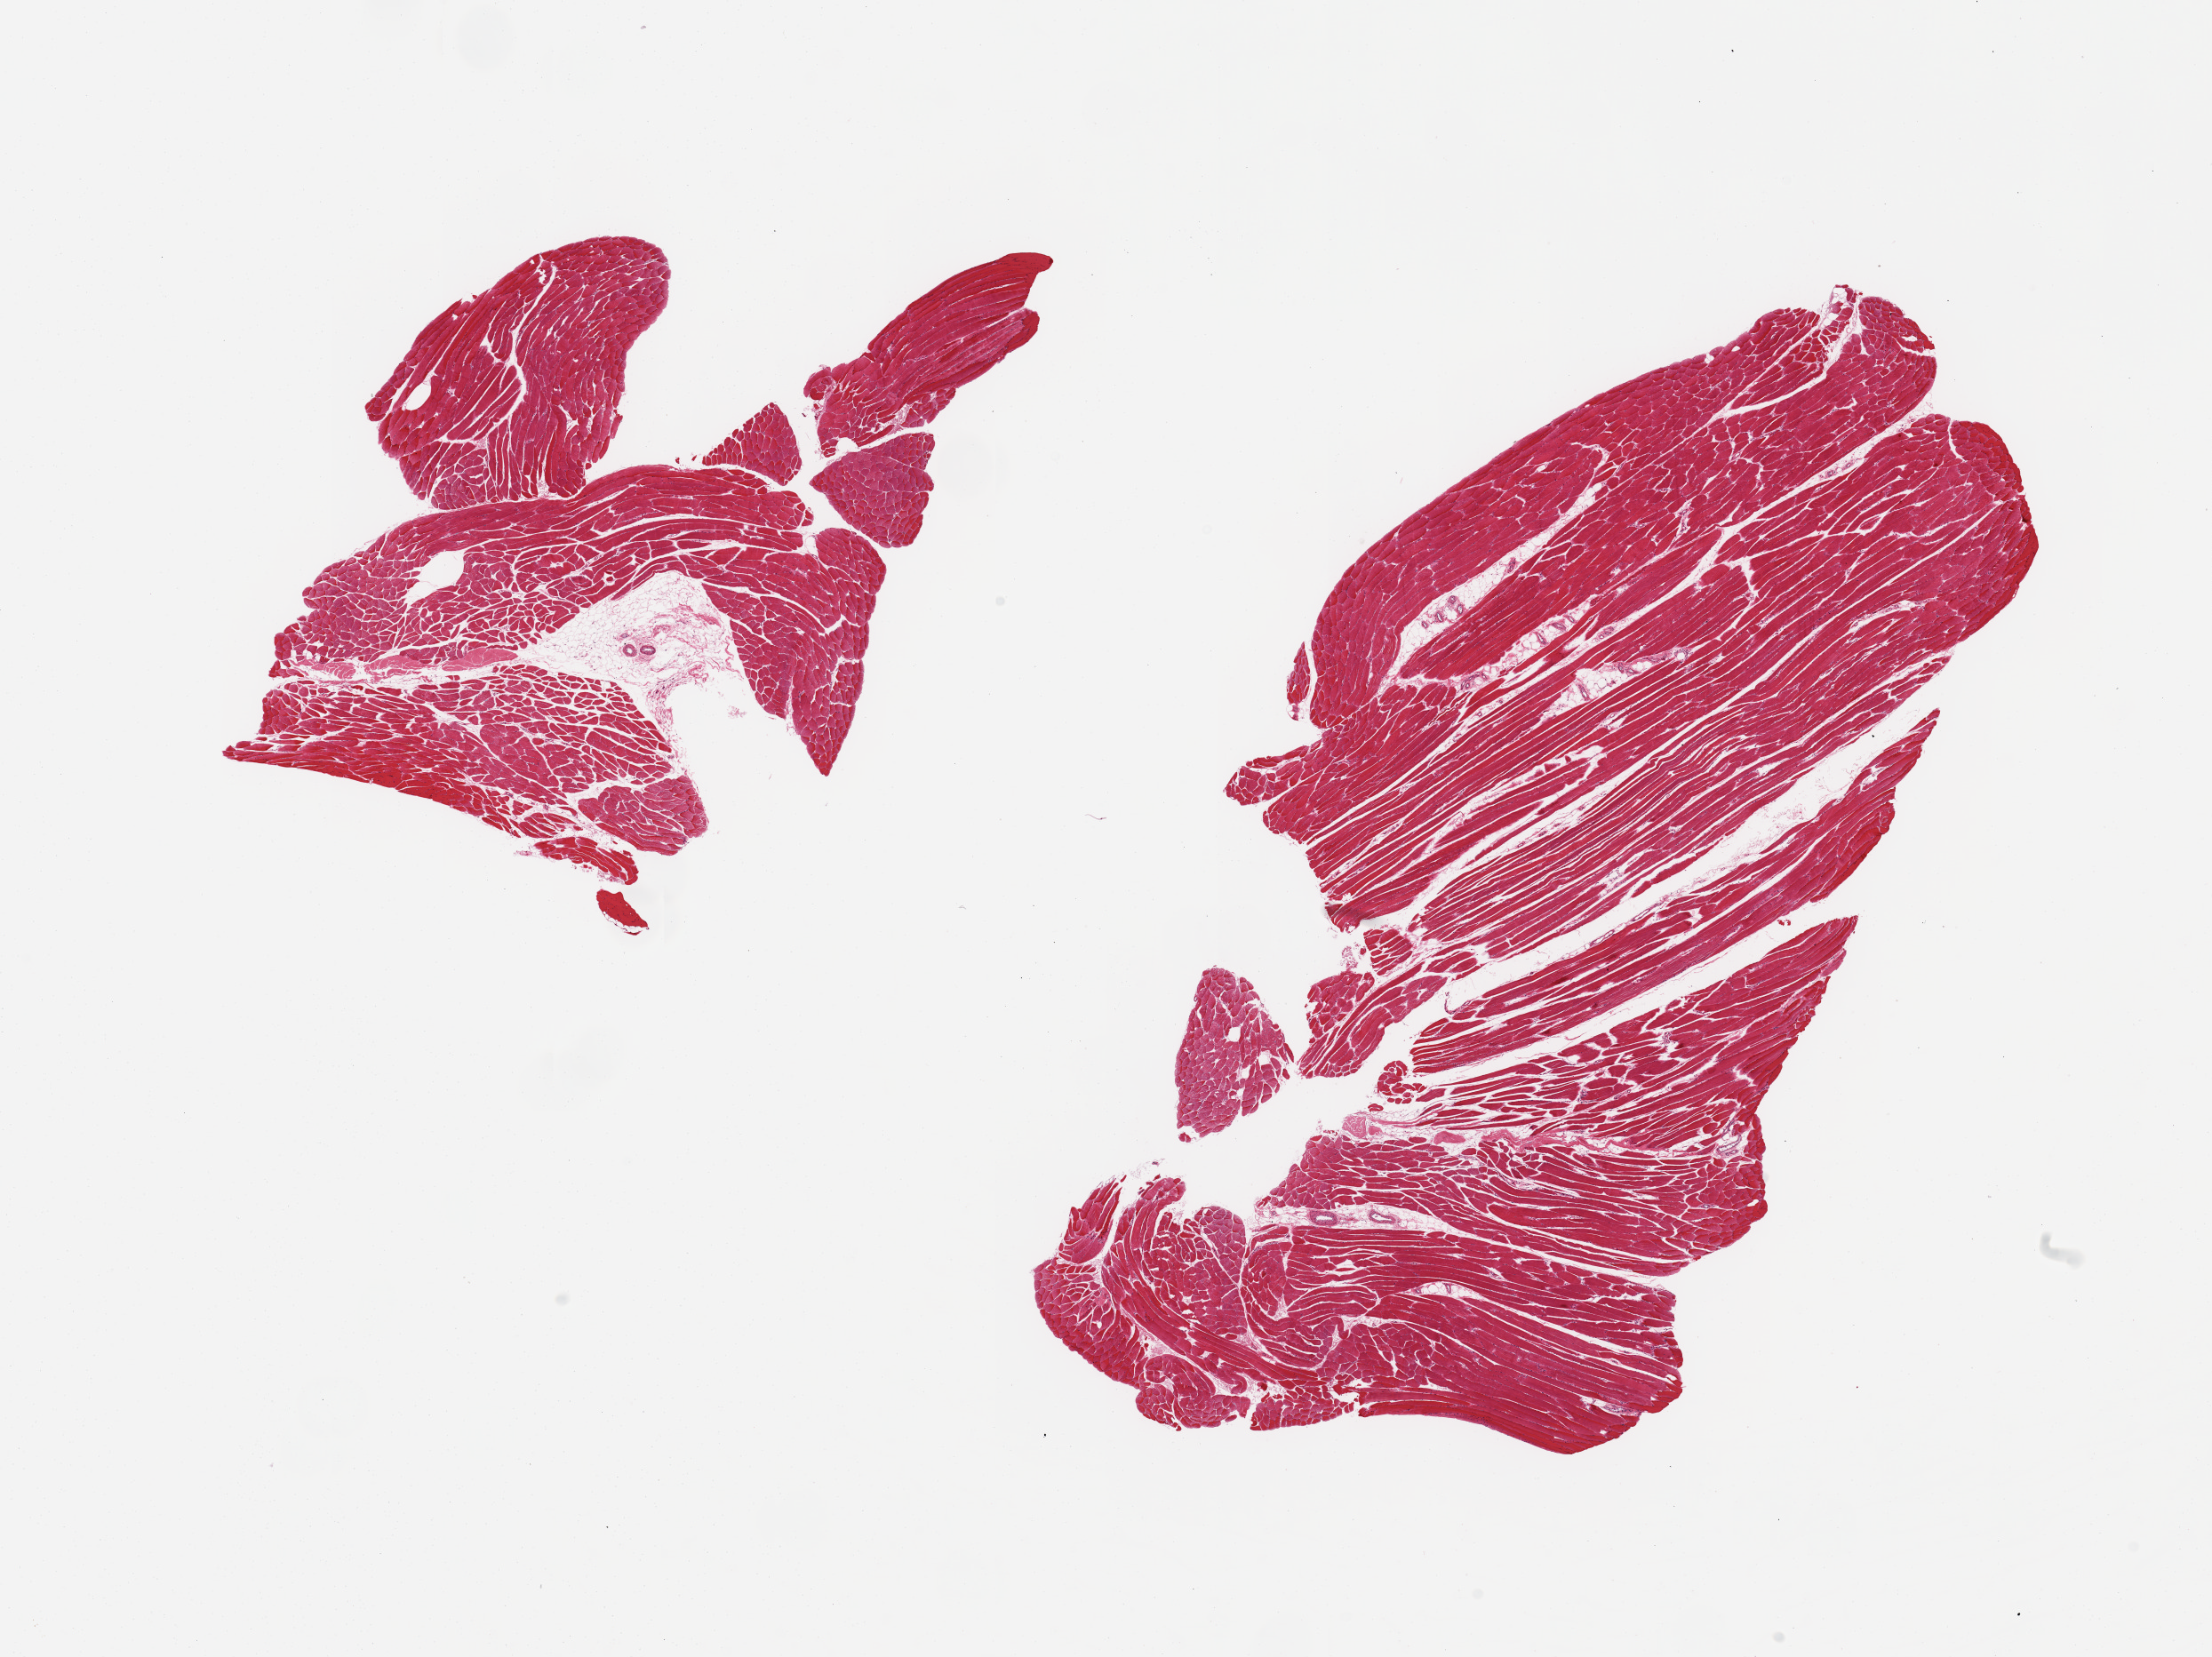
Digitized haematoxylin and eosin-stained section — shown as a low-resolution overview of the whole scanned area (about 19.7 x 14.8 mm, slide scanned at 20x); PAXgene-fixed paraffin-embedded (PFPE) section; target tissue: skeletal muscle; tissue donor sample. Donor: male.
Pathologist's review note for this sample: 2 pieces; includes up to ~10% internal fat.